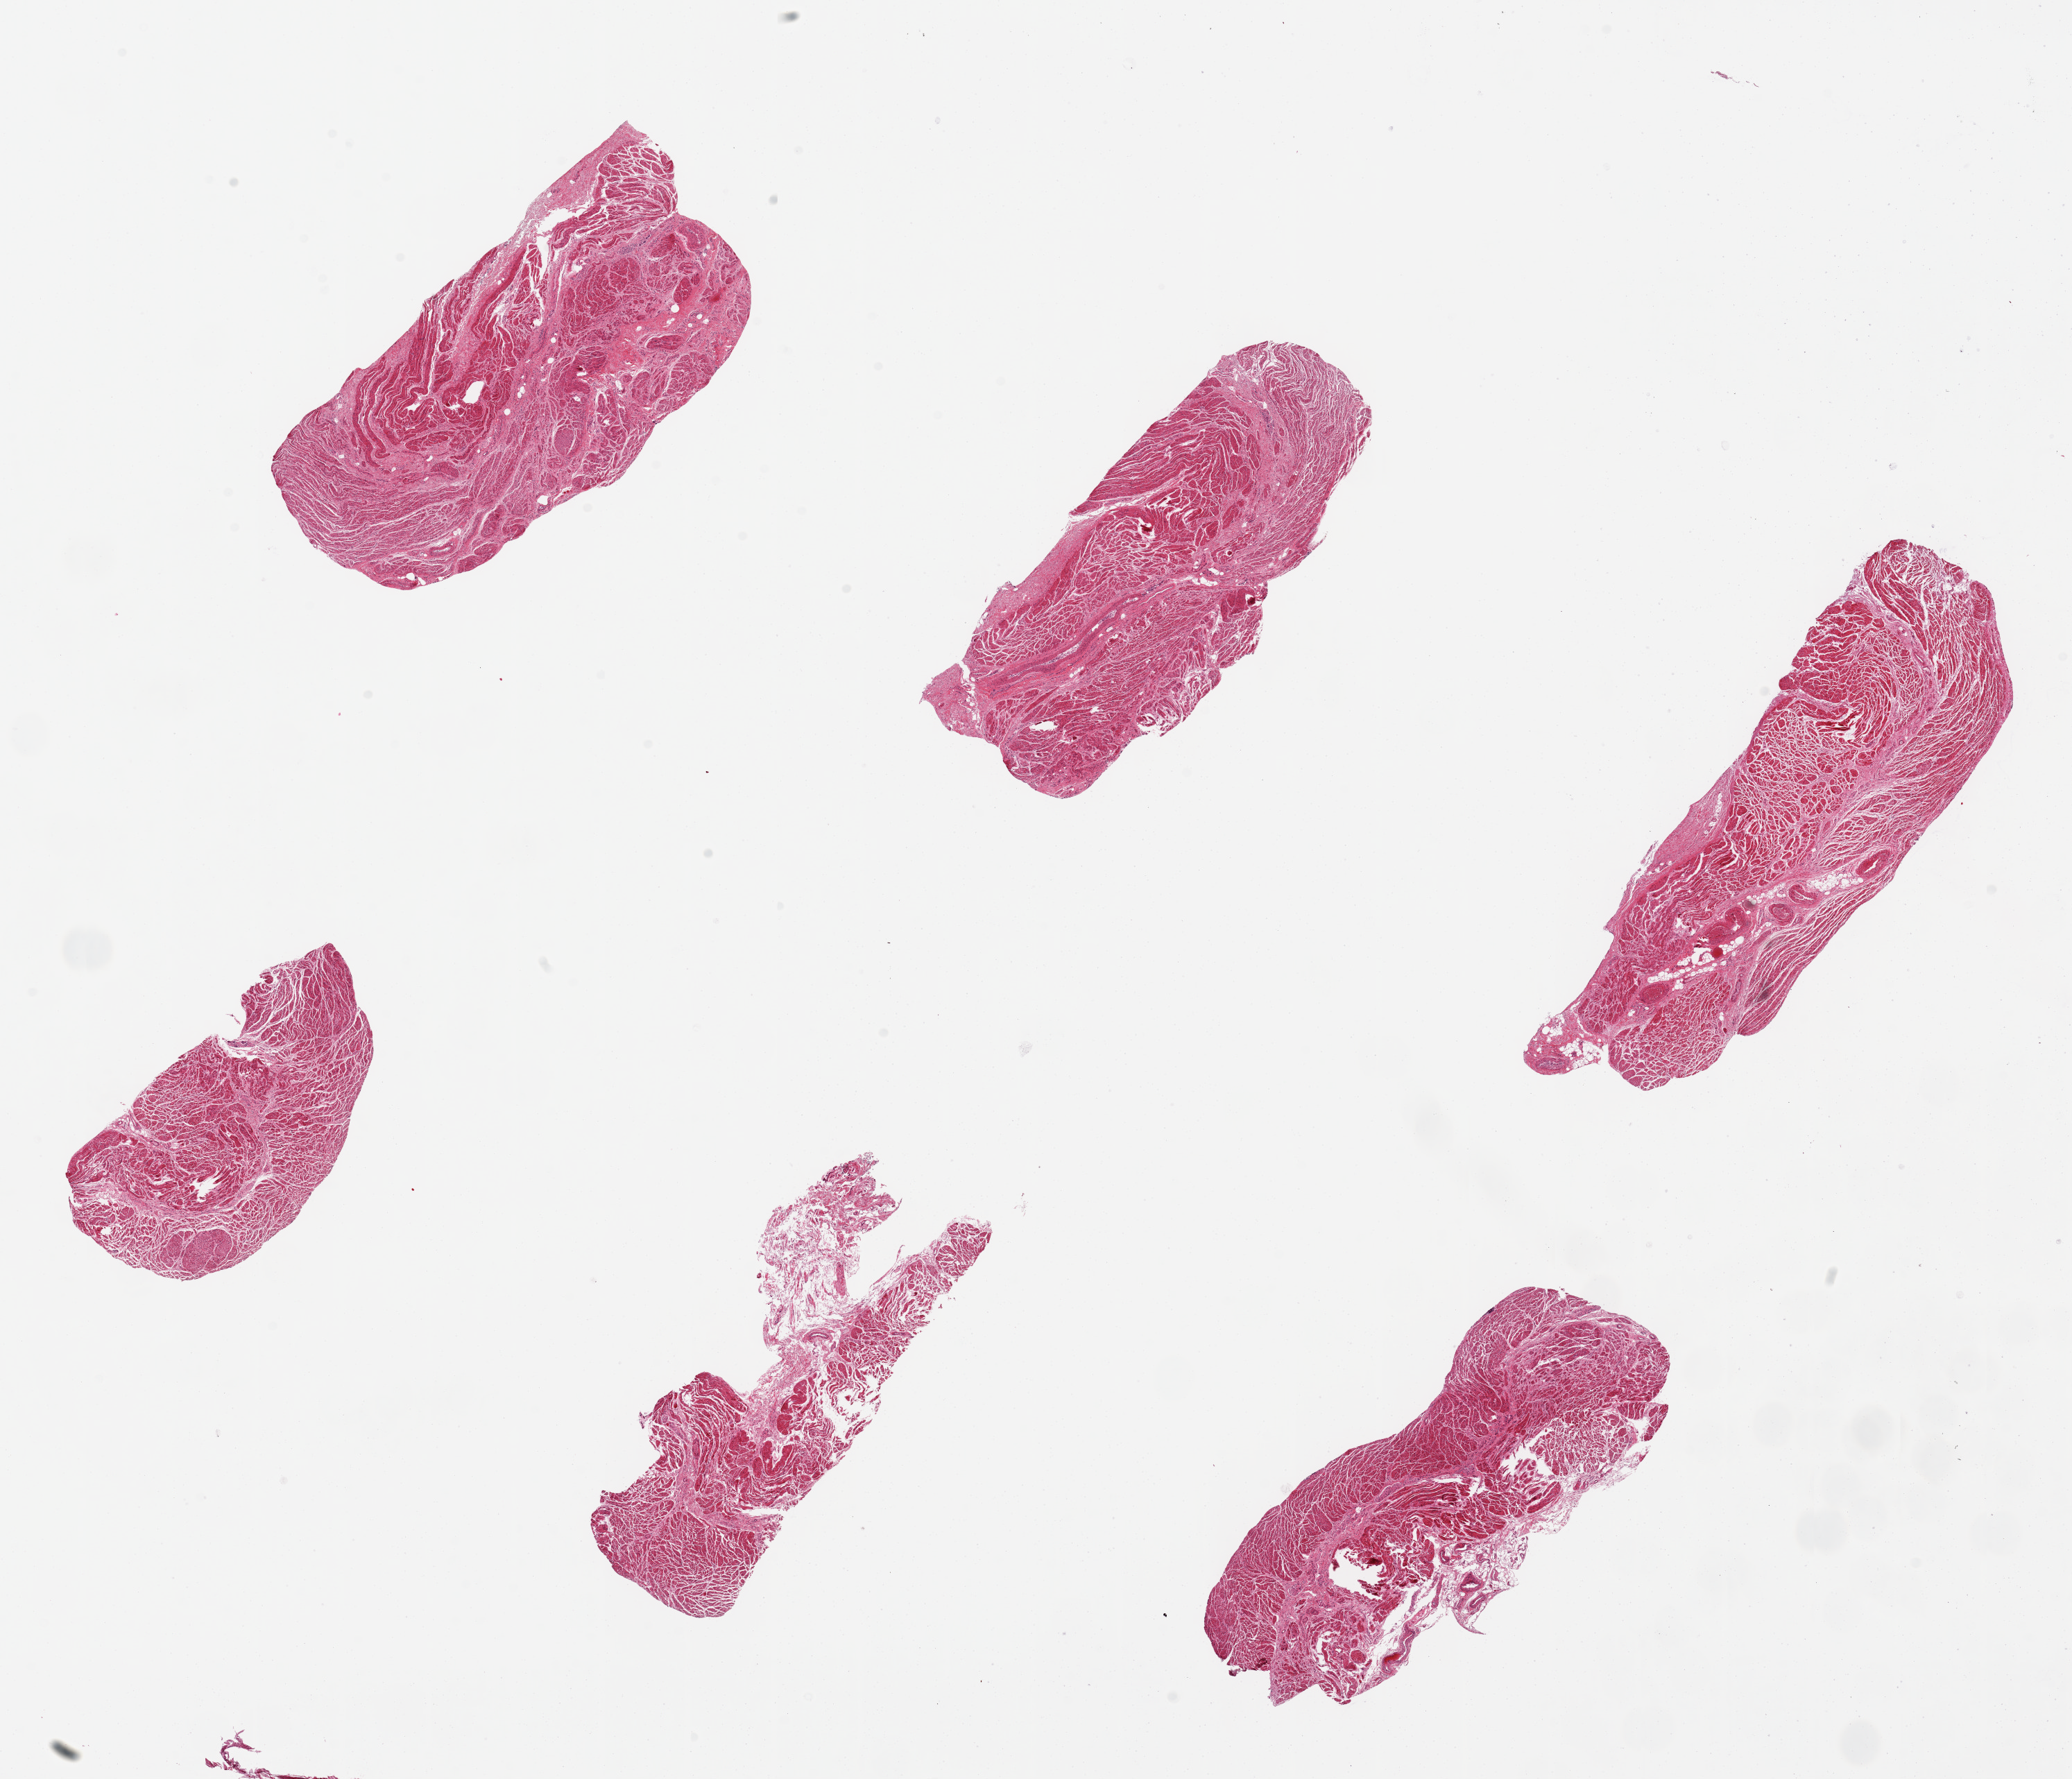
Digitized hematoxylin and eosin (H&E)-stained section, brightfield — whole scanned area (about 23.6 x 20.3 mm, slide scanned at 20x) shown as a low-resolution overview; PAXgene-fixed paraffin-embedded (PFPE) section; section of gastroesophageal junction (target tissue); tissue donor sample. Donor sex: male.
Reviewer comment on this tissue sample: 6 pieces. up to 7x2.5mm; all muscularis, good specimens.